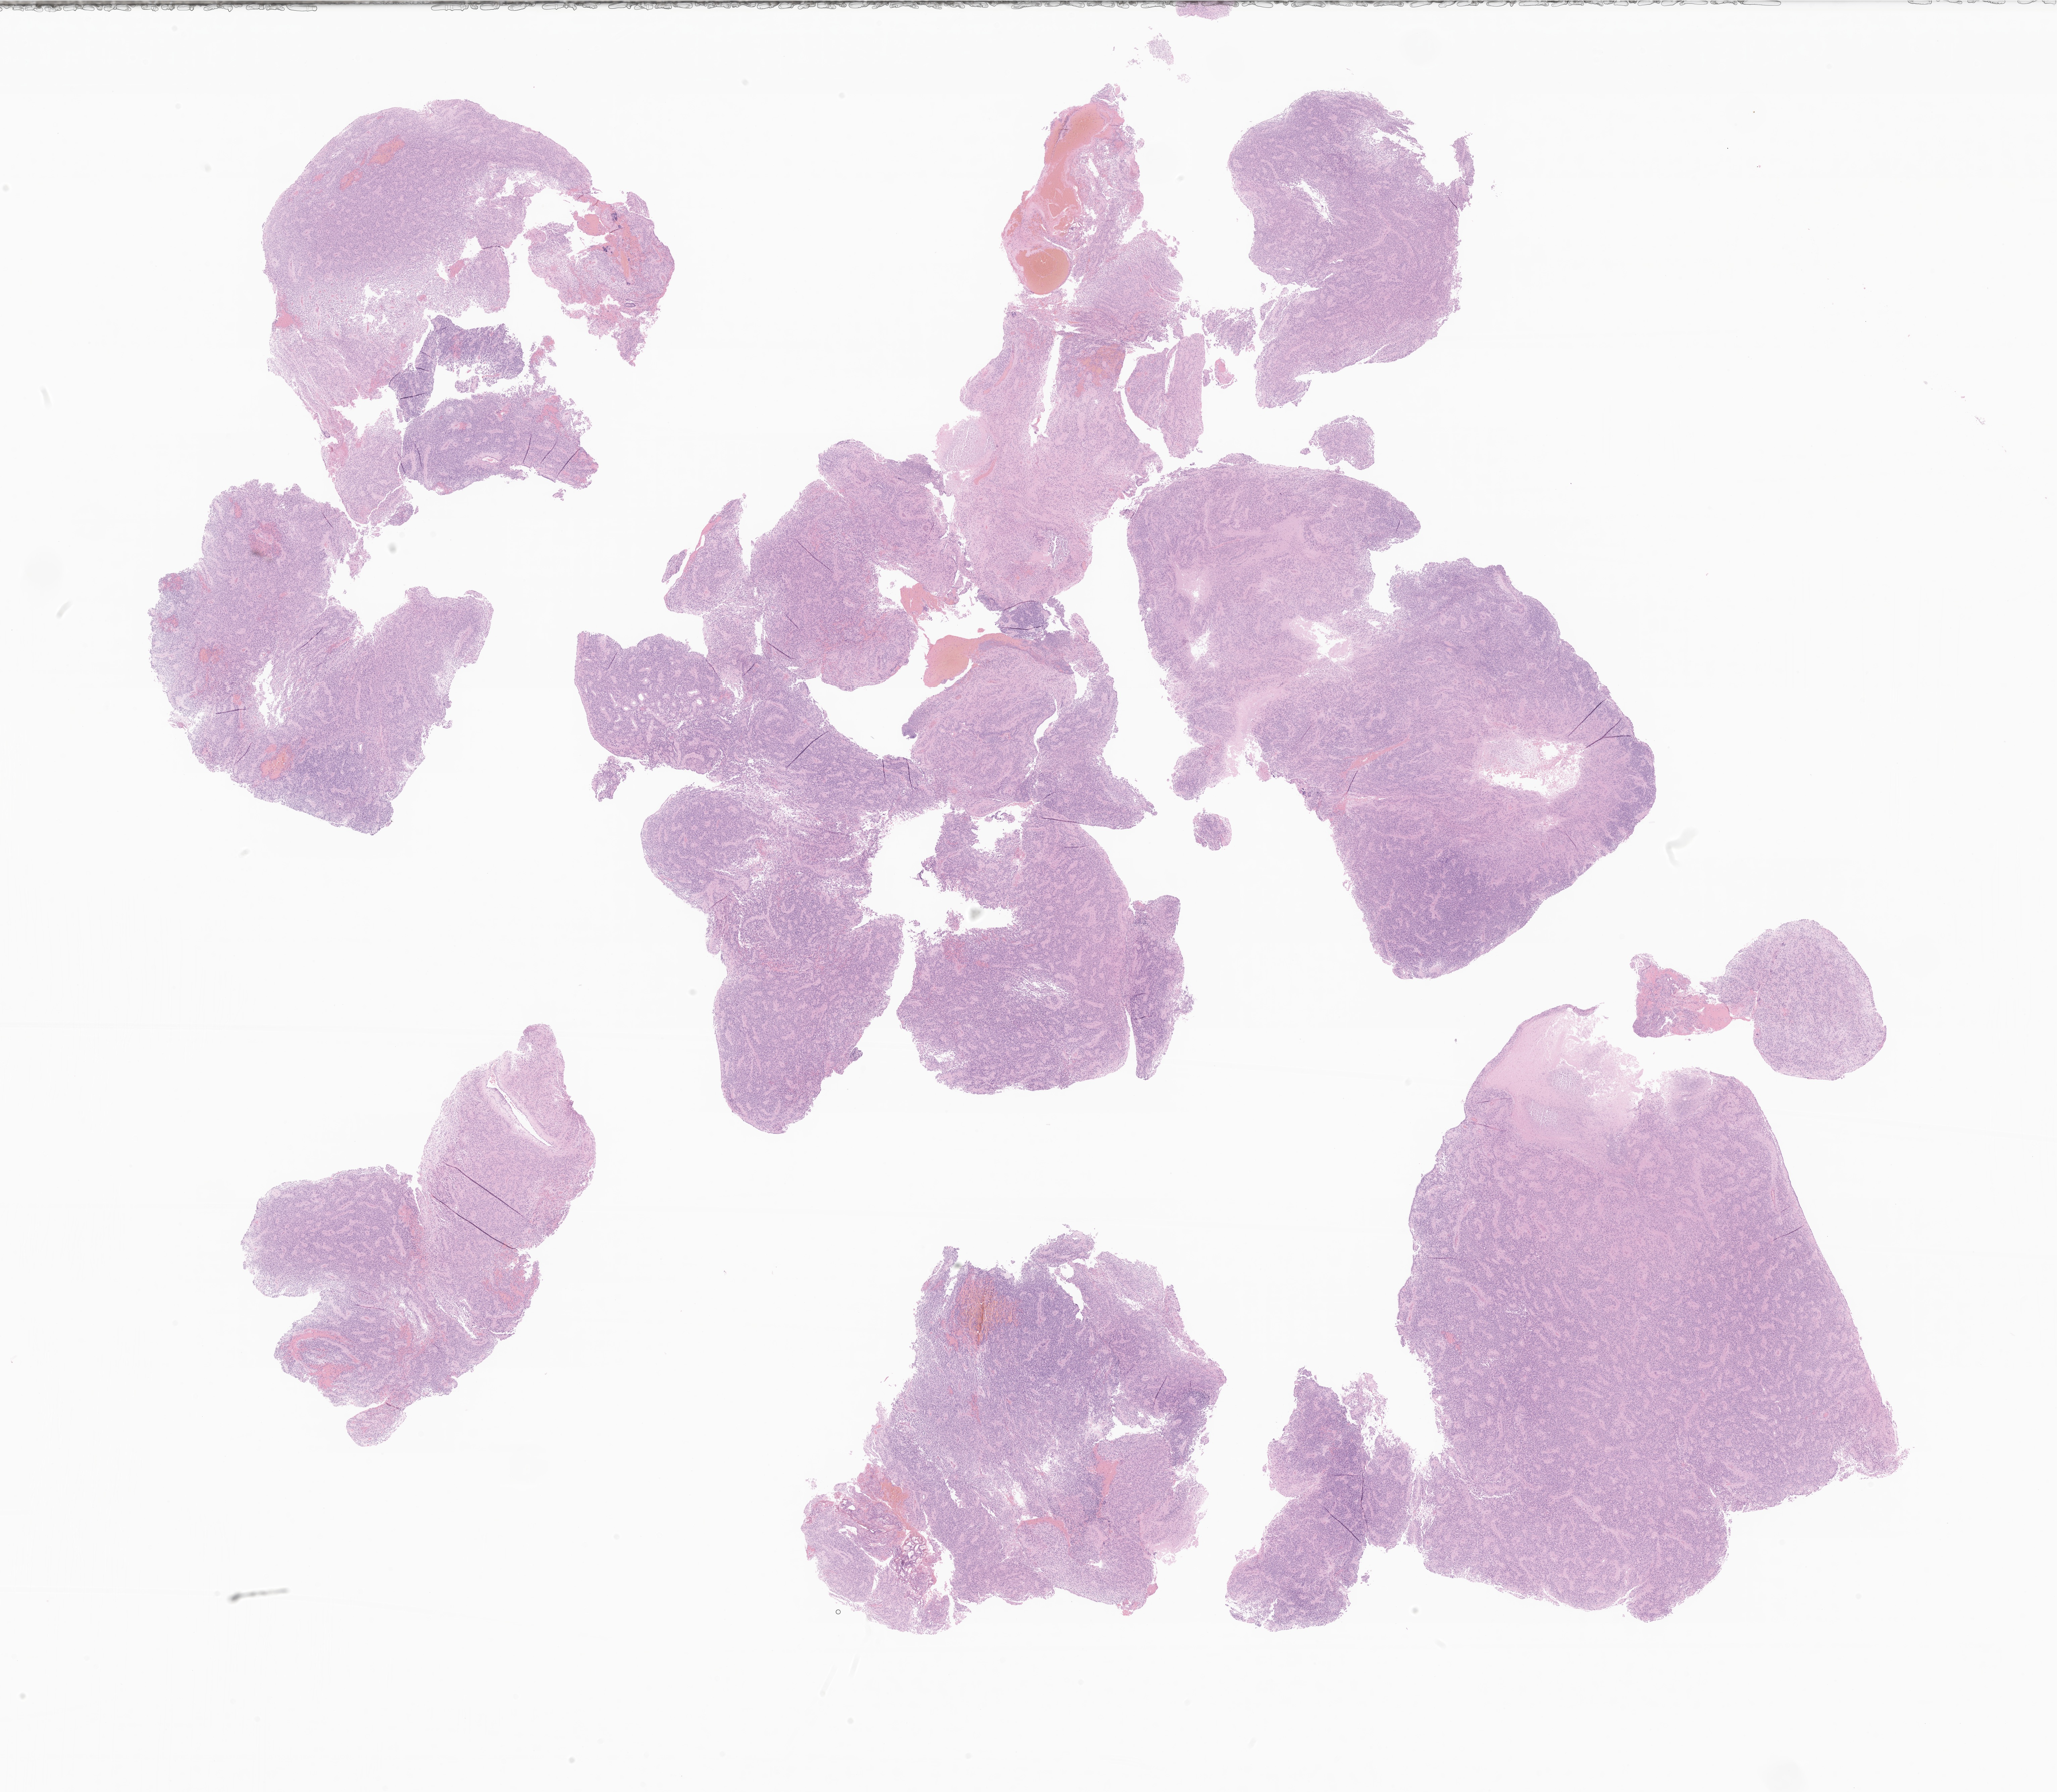
Digitized hematoxylin and eosin (H&E)-stained section of tumor tissue from the brain — low-resolution overview of the scanned area, about 25.8 x 22.5 mm; FFPE section. Patient: female, age 36 months.
- recorded diagnosis: Ependymoma, NOS